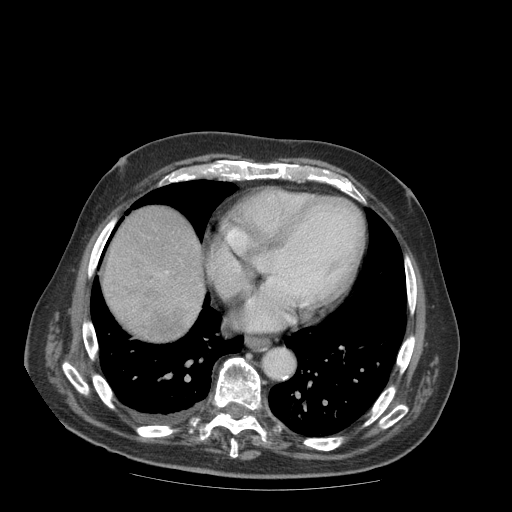
Contrast-enhanced abdominal CT (liver protocol), one axial slice. Slice 88 of 99 in the series (ordered by position). Soft-tissue window (W 400 / L 40 HU). 2.5 mm slice thickness. 512 × 512 image matrix, field of view 420 × 420 mm. Case-level facts recorded for this patient, not image findings: diagnosis: hepatocellular carcinoma (patient treated with transarterial chemoembolisation; whether this scan precedes or follows treatment is not stated here); TNM stage (as recorded): Stage-IIIB; Child-Pugh class: A; tumour differentiation: well differentiated; tumour nodularity: multinodular.
Annotated regions visible in this slice (semi-automatically segmented with operator editing):
- abdominal aorta: bounding box [x1, y1, x2, y2] px = [263, 349, 294, 378]
- liver parenchyma outside the tumour (the mass and vessels are separate outlines, so this box may not span the whole liver): [101, 206, 204, 328]
- mass: [102, 236, 202, 343]